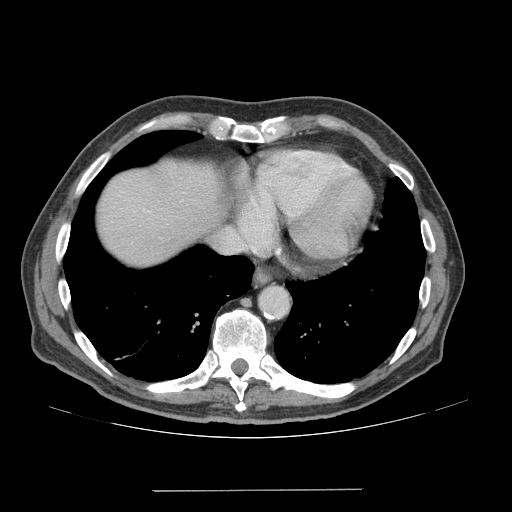
Contrast-enhanced abdominal CT (liver protocol), one axial slice; position 65 of 77 along the scan axis; reconstruction kernel STANDARD; 140 kVp; soft-tissue window (W 400 / L 40 HU); 2.5 mm slice thickness; 512 × 512 image matrix. From the clinical record (not read from this slice): diagnosis: hepatocellular carcinoma (patient treated with transarterial chemoembolisation; whether this scan precedes or follows treatment is not stated here); TNM stage (as recorded): Stage-IVA; Child-Pugh class: A; tumour differentiation: well differentiated; tumour nodularity: uninodular.
Structures marked on this image (semi-automatically segmented with operator editing):
- abdominal aorta: bounding box (x1, y1, x2, y2) in pixels: (260, 287, 287, 315)
- liver parenchyma outside the tumour (the mass and vessels are separate outlines, so this box may not span the whole liver): (98, 160, 222, 266)